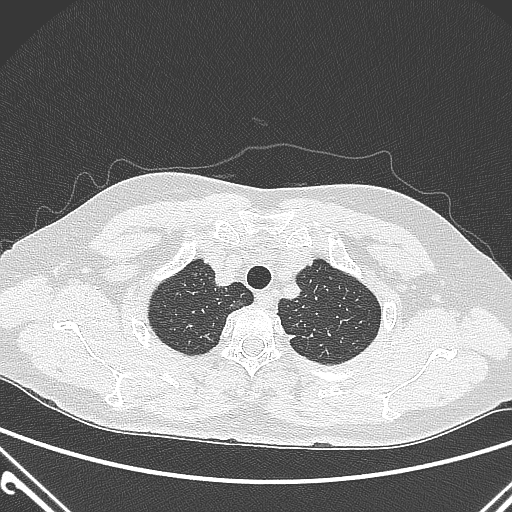
Chest CT, one axial slice; position 248 of 300 along the scan axis; 120 kVp; lung window (W 1500 / L -600 HU); 1 mm slice thickness; 512 × 512 image matrix, field of view 350 × 350 mm. Female patient, age 54 years. From the clinical record (not read from this slice): clinical TNM (as recorded): T1a N0 M0.
Outlined on this slice (rectangle marked by the reading radiologist):
- lung tumour (recorded histology: adenocarcinoma): bounding box (x1, y1, x2, y2) in pixels: (228, 292, 250, 313)